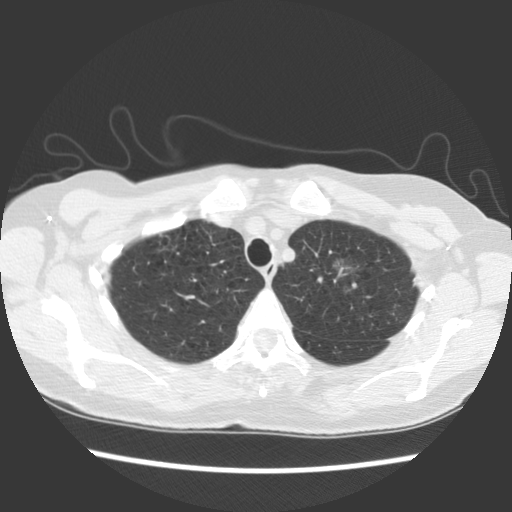
Low-dose screening chest CT, axial slice. Baseline screening round. Lung window (W 1500 / L -600 HU). 2.5 mm slice thickness. Slice 102 of 129 in the series. Female, age 65 years at enrolment. Former smoker at enrolment.
Expert-annotated lung lesion, bounding box [x1, y1, x2, y2] px = [311, 242, 381, 299]. Reader record for this screening exam (exam-level; its link to the box is not recorded): non-calcified nodule or mass ≥4 mm, left upper lobe, 11 × 10 mm, poorly defined margins, ground glass attenuation. Lung cancer was diagnosed 810 days after this screen (after the third annual screen): adenocarcinoma, NOS, left upper lobe, moderately differentiated (G2), stage IA (AJCC 6th edition), 30 mm at pathology.